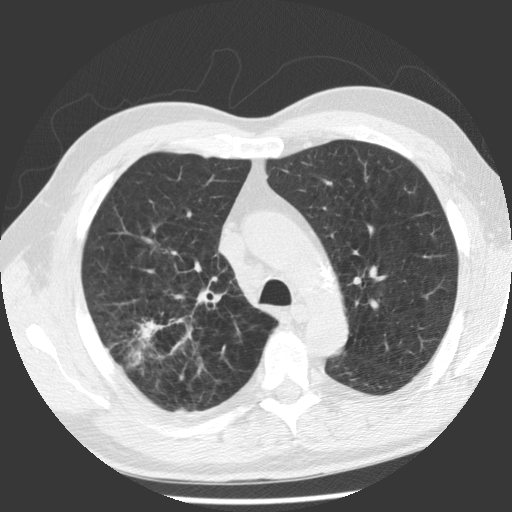
Low-dose screening chest CT, one axial slice. Slice 79 of 112 in the series (ordered by position). Reconstruction kernel STANDARD. 140 kVp. Lung window (W 1500 / L -600 HU). 2.5 mm slice thickness. 512 × 512 image matrix, field of view 344 × 344 mm.
Annotated regions visible in this slice (outlined manually by an expert reader):
- lesion 1 (tumor, upper lobe of right lung): bounding box (x1, y1, x2, y2) in pixels: (138, 321, 163, 339)